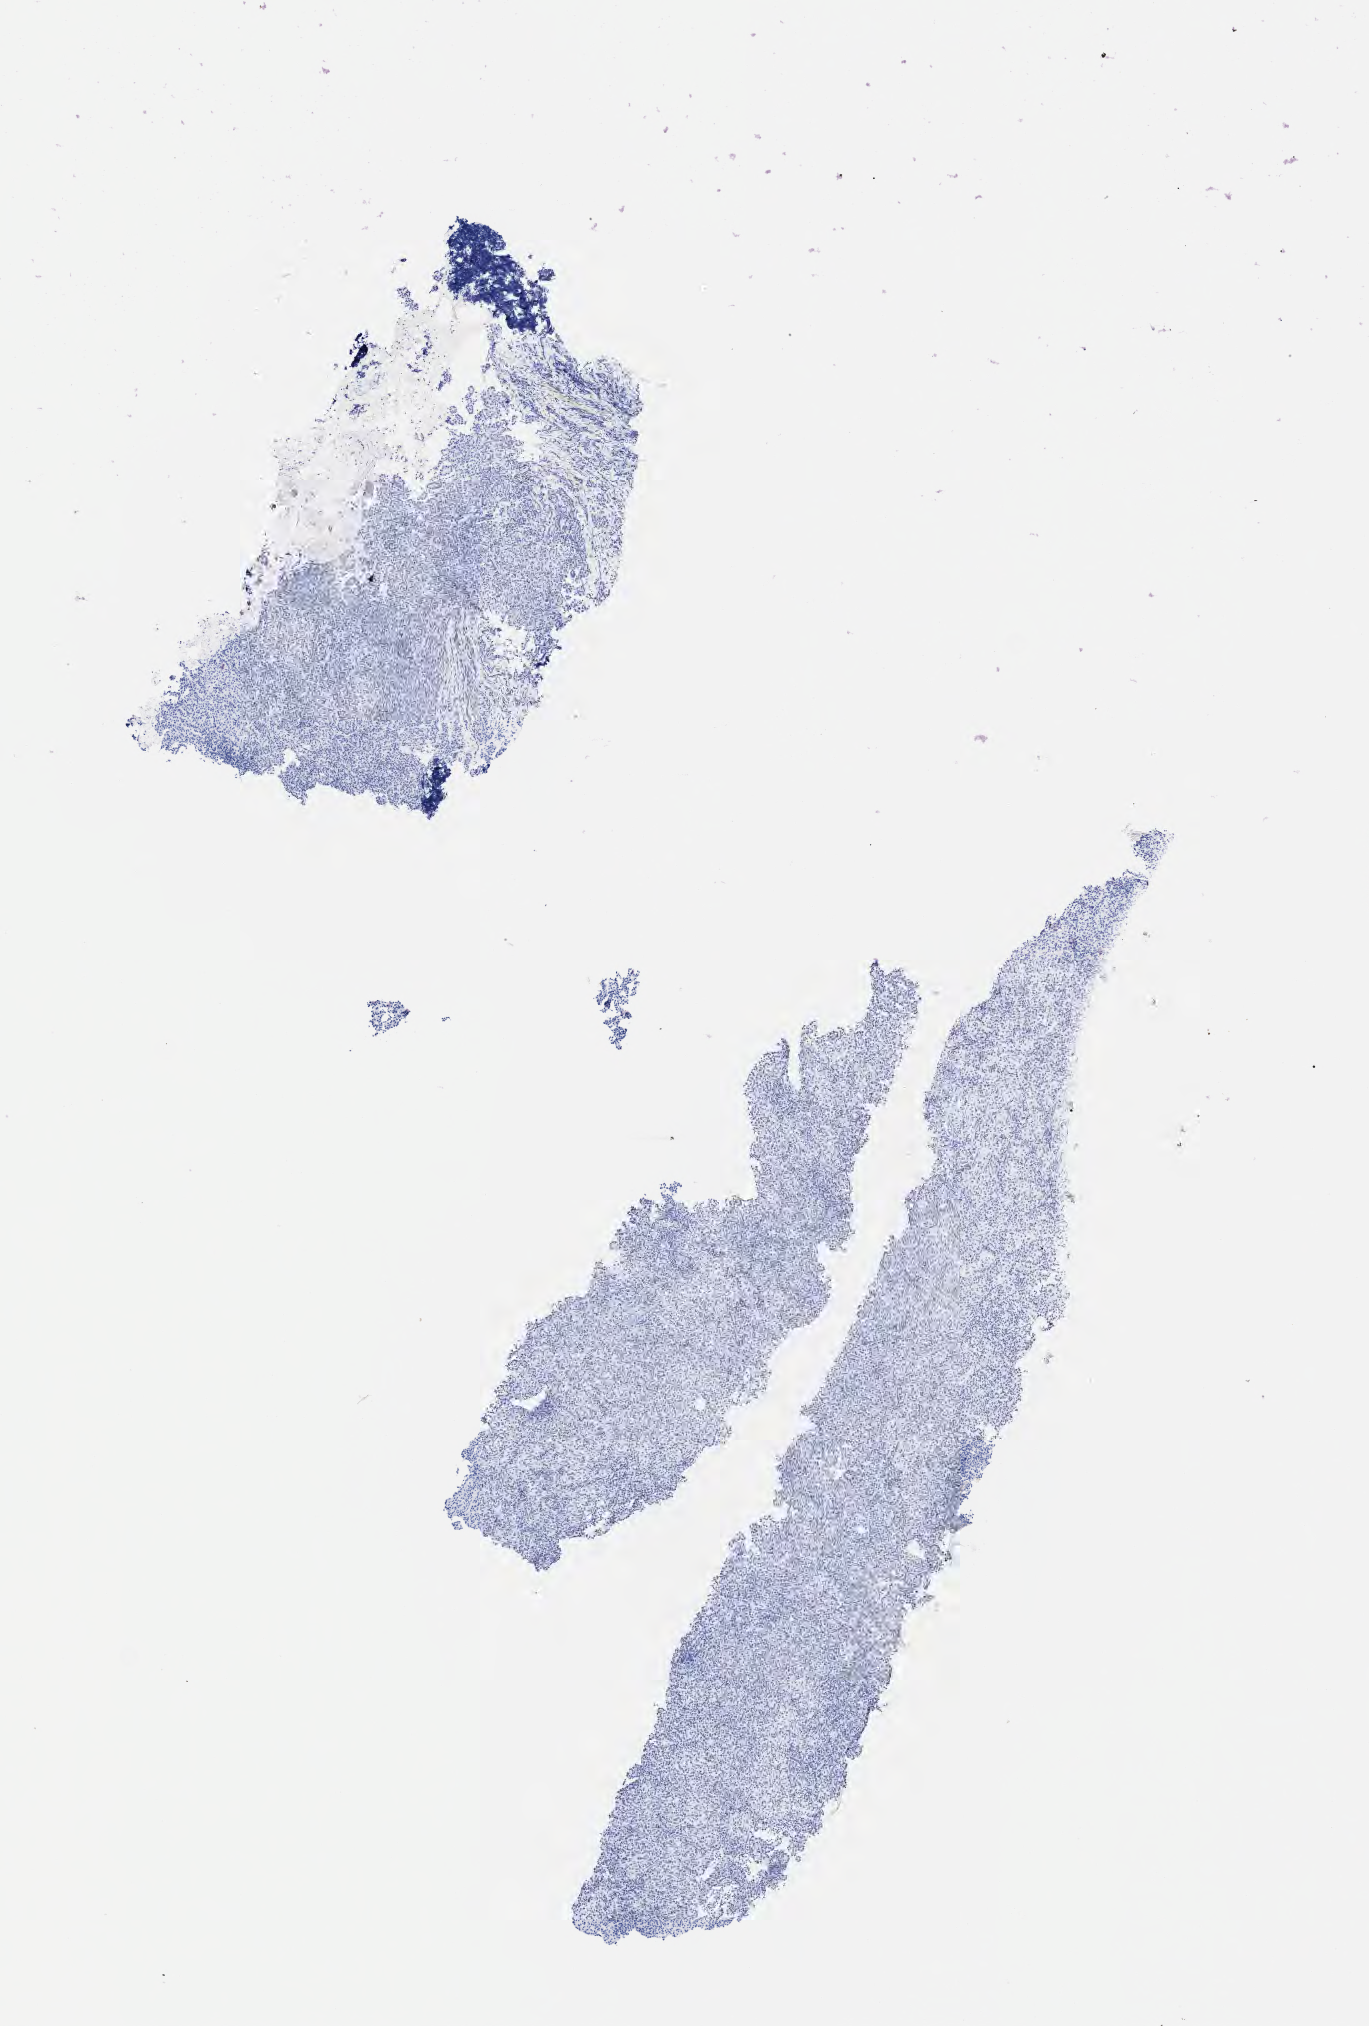
Whole-slide image, immunohistochemical stain for chromogranin, low-resolution overview of the scanned area, about 5.5 x 8.2 mm, specimen: tumor tissue, anatomic site: lung (left). Patient: female, age 65 years.
Diagnosis: Non-small cell carcinoma.